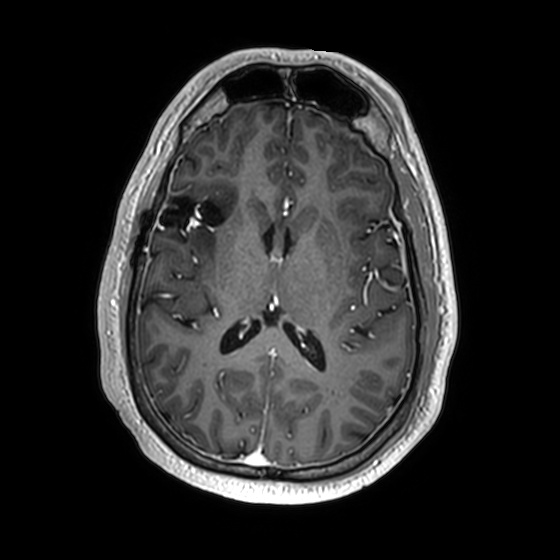
Brain MRI from a brain-tumour surgery series, one axial slice; T1-weighted post-contrast; 1 mm slice thickness; 560 × 560 image matrix, field of view 256 × 256 mm. Case-level facts recorded for this patient, not image findings: histopathology: Astrocytoma; WHO grade: 2; IDH mutation: yes; tumour location: Right Insular.
Annotated regions visible in this slice (outlined manually by an expert reader):
- previous resection cavity: bounding box <160,196,224,227> (left, top, right, bottom; pixels)